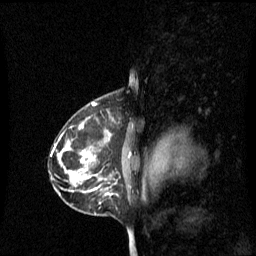
Breast MRI (dynamic contrast-enhanced), one sagittal slice; position 43 of 60 along the scan axis; dynamic contrast-enhanced series, image 2 of 3 at this slice position (ordered by acquisition); 1.5 T; TE 4.2 ms, TR 8.4 ms; 256 × 256 image matrix, field of view 240 × 240 mm. Female patient, age 42 years. Case-level facts recorded for this patient, not image findings: setting: breast cancer imaged before/during neoadjuvant chemotherapy; receptor status: HR-positive, HER2-negative.
Annotated regions visible in this slice (semi-automatically segmented with operator editing):
- analysis volume of interest (the breast-tissue region the enhancement analysis was run in; not a lesion): bounding box (x1, y1, x2, y2) in pixels: (68, 110, 135, 195)
- tumour enhancement mask (voxels above the 70 % enhancement threshold inside the analysis volume of interest): (82, 152, 95, 191)